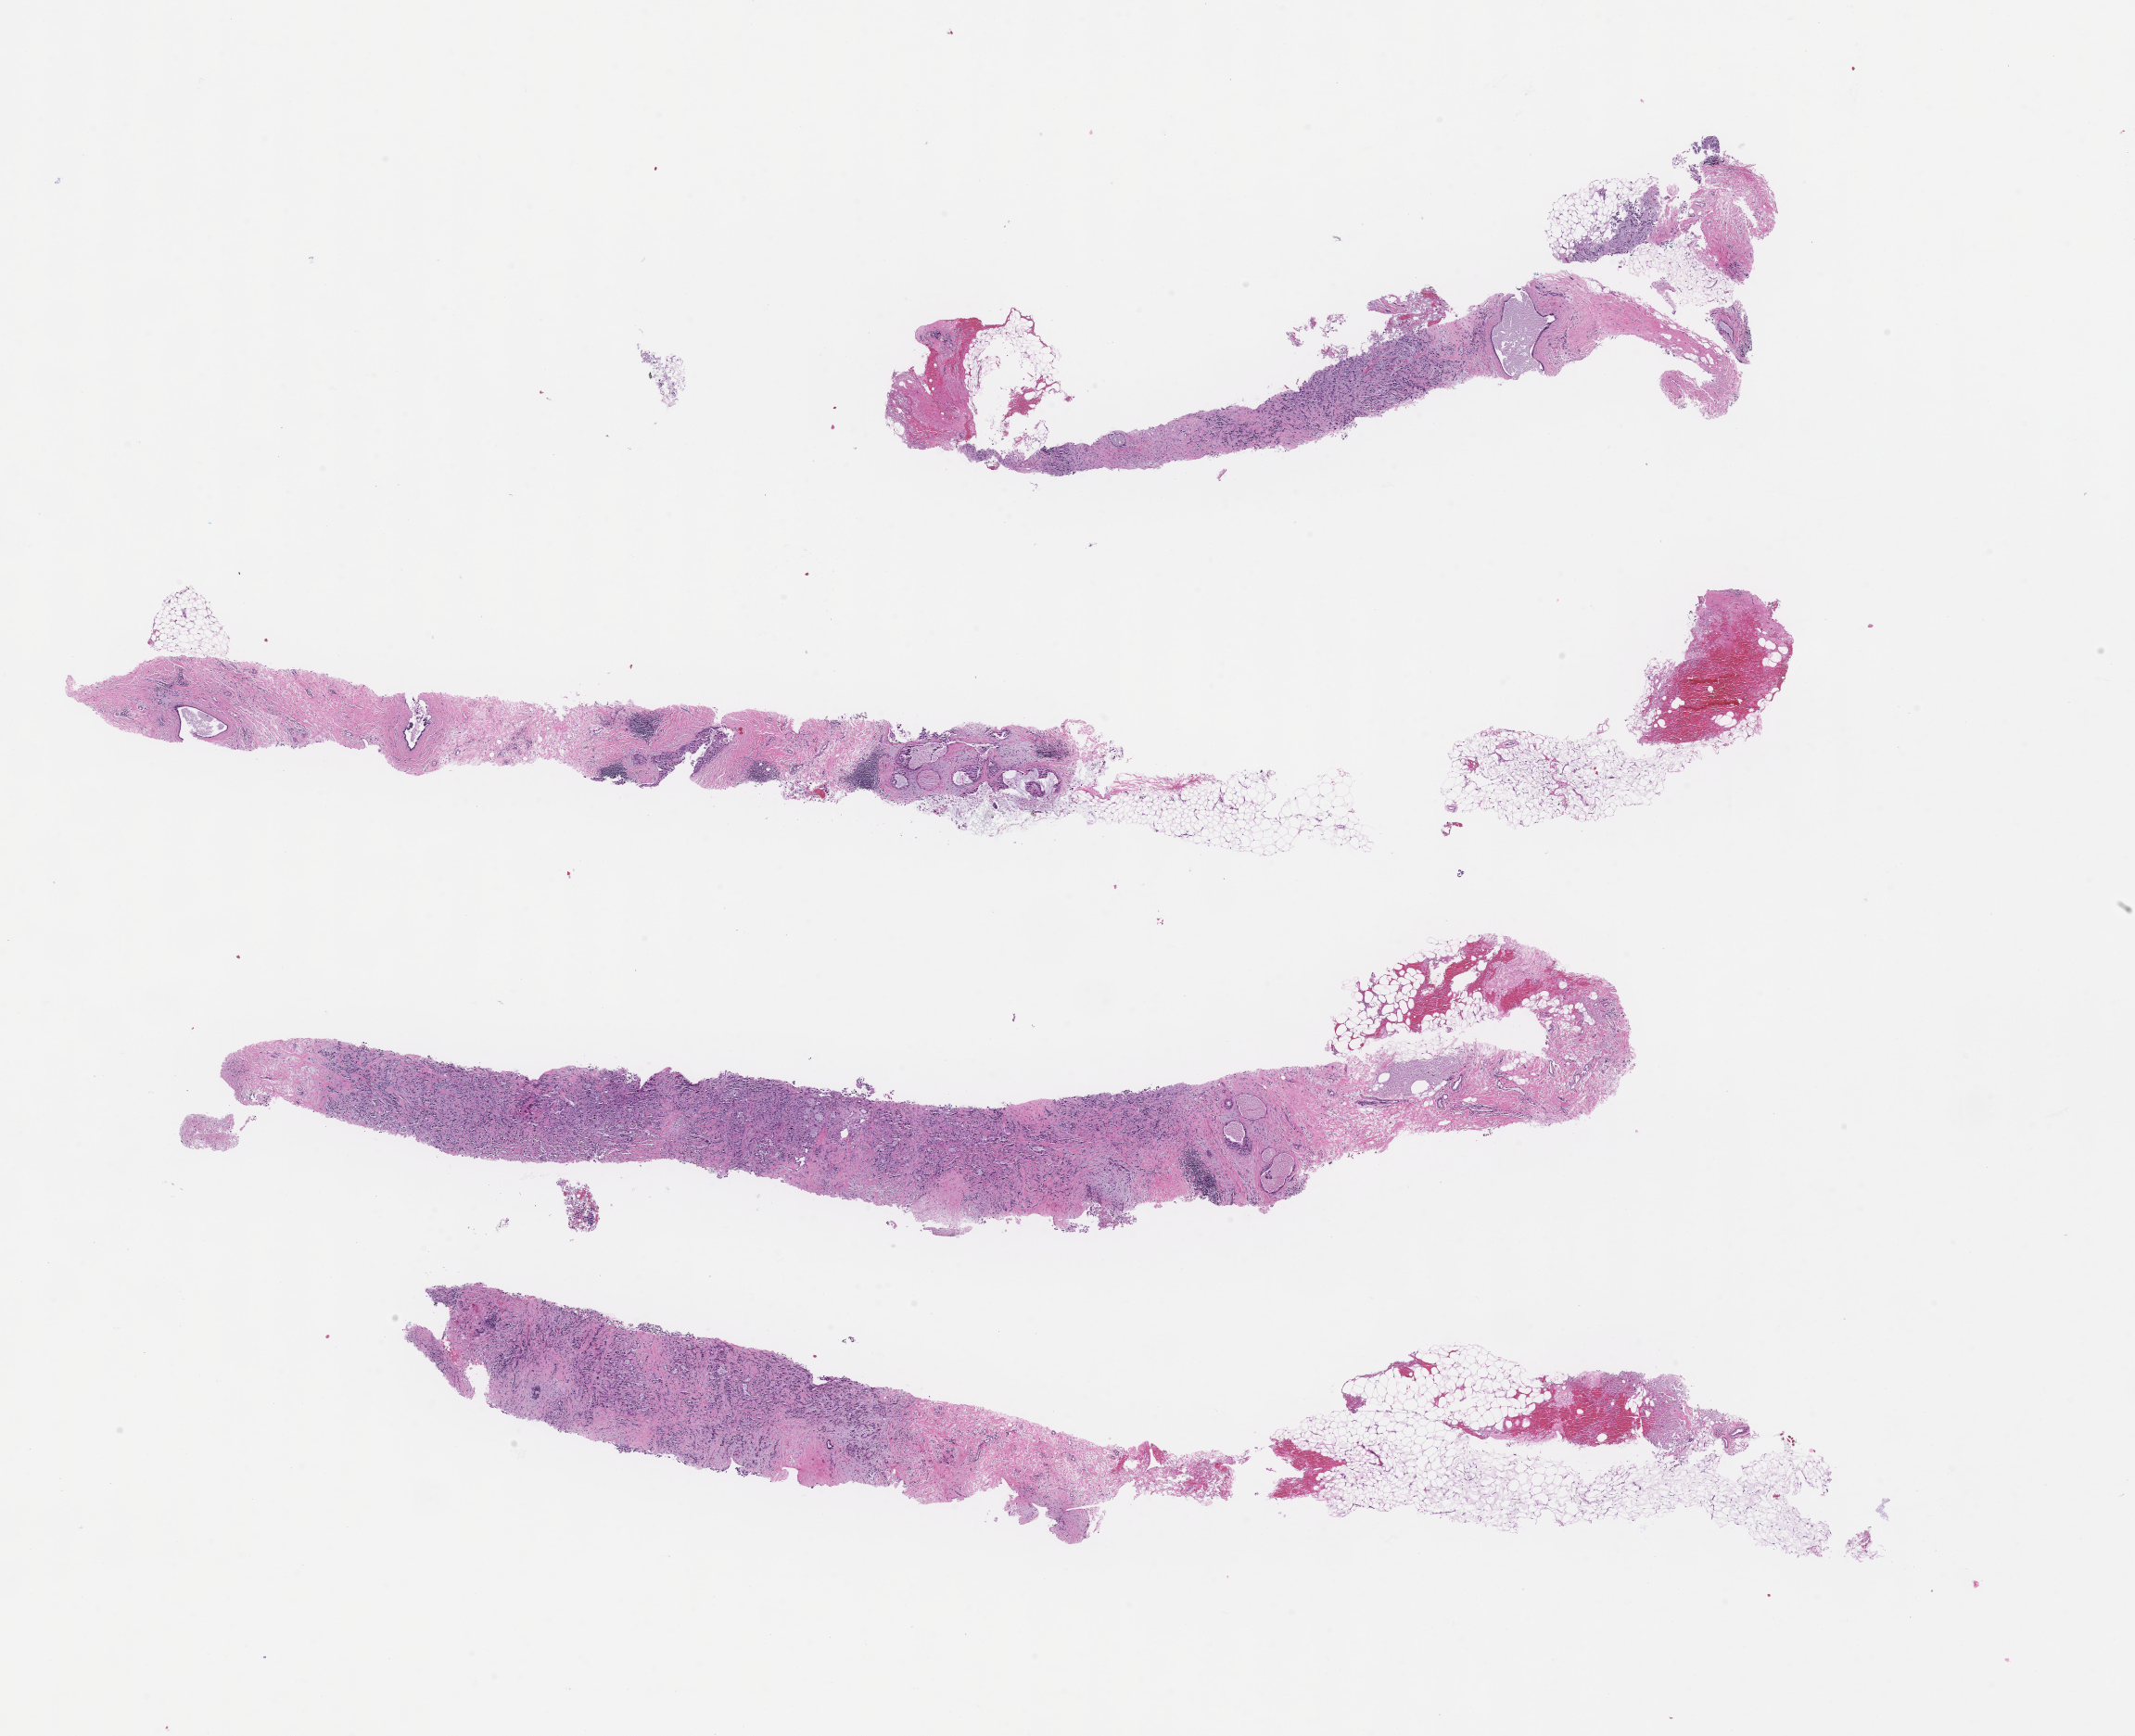
Digitized H&E-stained section — a low-resolution overview of the entire scanned area, about 18.6 x 15.1 mm, FFPE section, site: breast. Female patient.
* this section: primary tumour tissue
* diagnosis: Invasive Breast Carcinoma